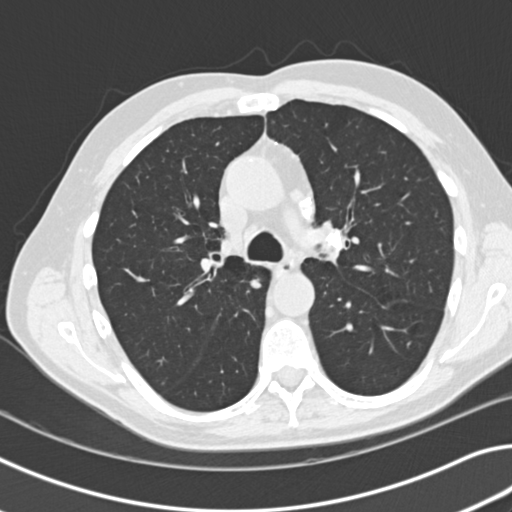
Low-dose screening chest CT, axial slice, first (baseline) screen, lung window (W 1500 / L -600 HU), 2 mm slice thickness, standard (soft-tissue) reconstruction kernel (B30f), slice 57 of 154 in the series. Male, age 67 years at enrolment.
Expert-annotated lung lesion, bounding box <218,266,279,310> (left, top, right, bottom; pixels). No non-calcified nodule or mass ≥4 mm was recorded by the screening reader at this exam.